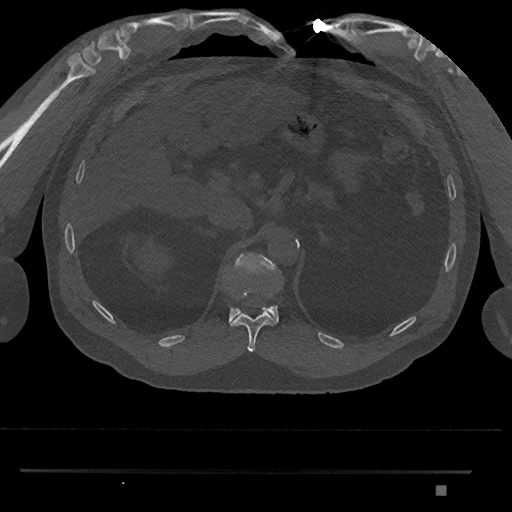
CT including the spine, one axial slice; position 924 of 1134 along the scan axis; bone window (W 1800 / L 400 HU); 0.5 mm slice thickness; 512 × 512 image matrix, field of view 429 × 429 mm. Patient: male, 65 years. Case-level facts recorded for this patient, not image findings: primary cancer: prostate.
Annotated regions visible in this slice (semi-automatically segmented with operator editing):
- T11 vertebra: bounding box <230,292,278,352> (left, top, right, bottom; pixels)
- T12 vertebra: <229,252,279,323>